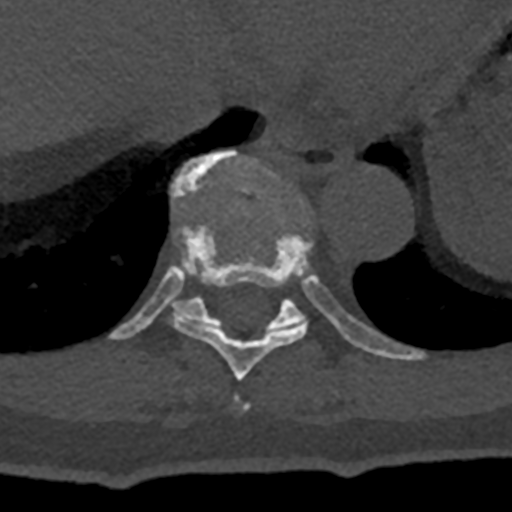
CT including the spine, one axial slice. Slice 636 of 797 in the series (ordered by position). Reconstruction kernel Br40s/3. 120 kVp. Bone window (W 1800 / L 400 HU). 0.5 mm slice thickness. 512 × 512 image matrix, field of view 160 × 160 mm. Patient: male, 74 years. From the clinical record (not read from this slice): primary cancer: renal; vertebrae with lytic lesions (as recorded): T10, L1, L2, L3, L4, L5.
Annotated regions visible in this slice (semi-automatic segmentation, software-assisted and operator-edited):
- T10 vertebra: bounding box (x1, y1, x2, y2) in pixels: (108, 150, 426, 361)
- T8 vertebra: (242, 403, 250, 409)
- T9 vertebra: (170, 226, 308, 381)